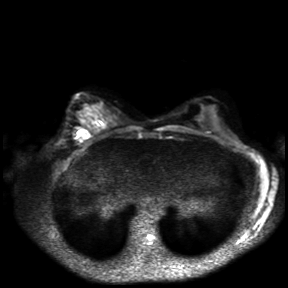
Breast MRI, one axial slice; slice 18 of 30 in the series (ordered by position); diffusion-weighted series; image 2 of 4 stored at this slice position (different b-values; order by instance number); 3 T; 4 mm slice thickness; 288 × 288 image matrix, field of view 360 × 360 mm. Female patient.
Structures marked on this image (expert manual segmentation):
- tumour on diffusion-weighted imaging: box from (x=76, y=130) to (x=89, y=140) px